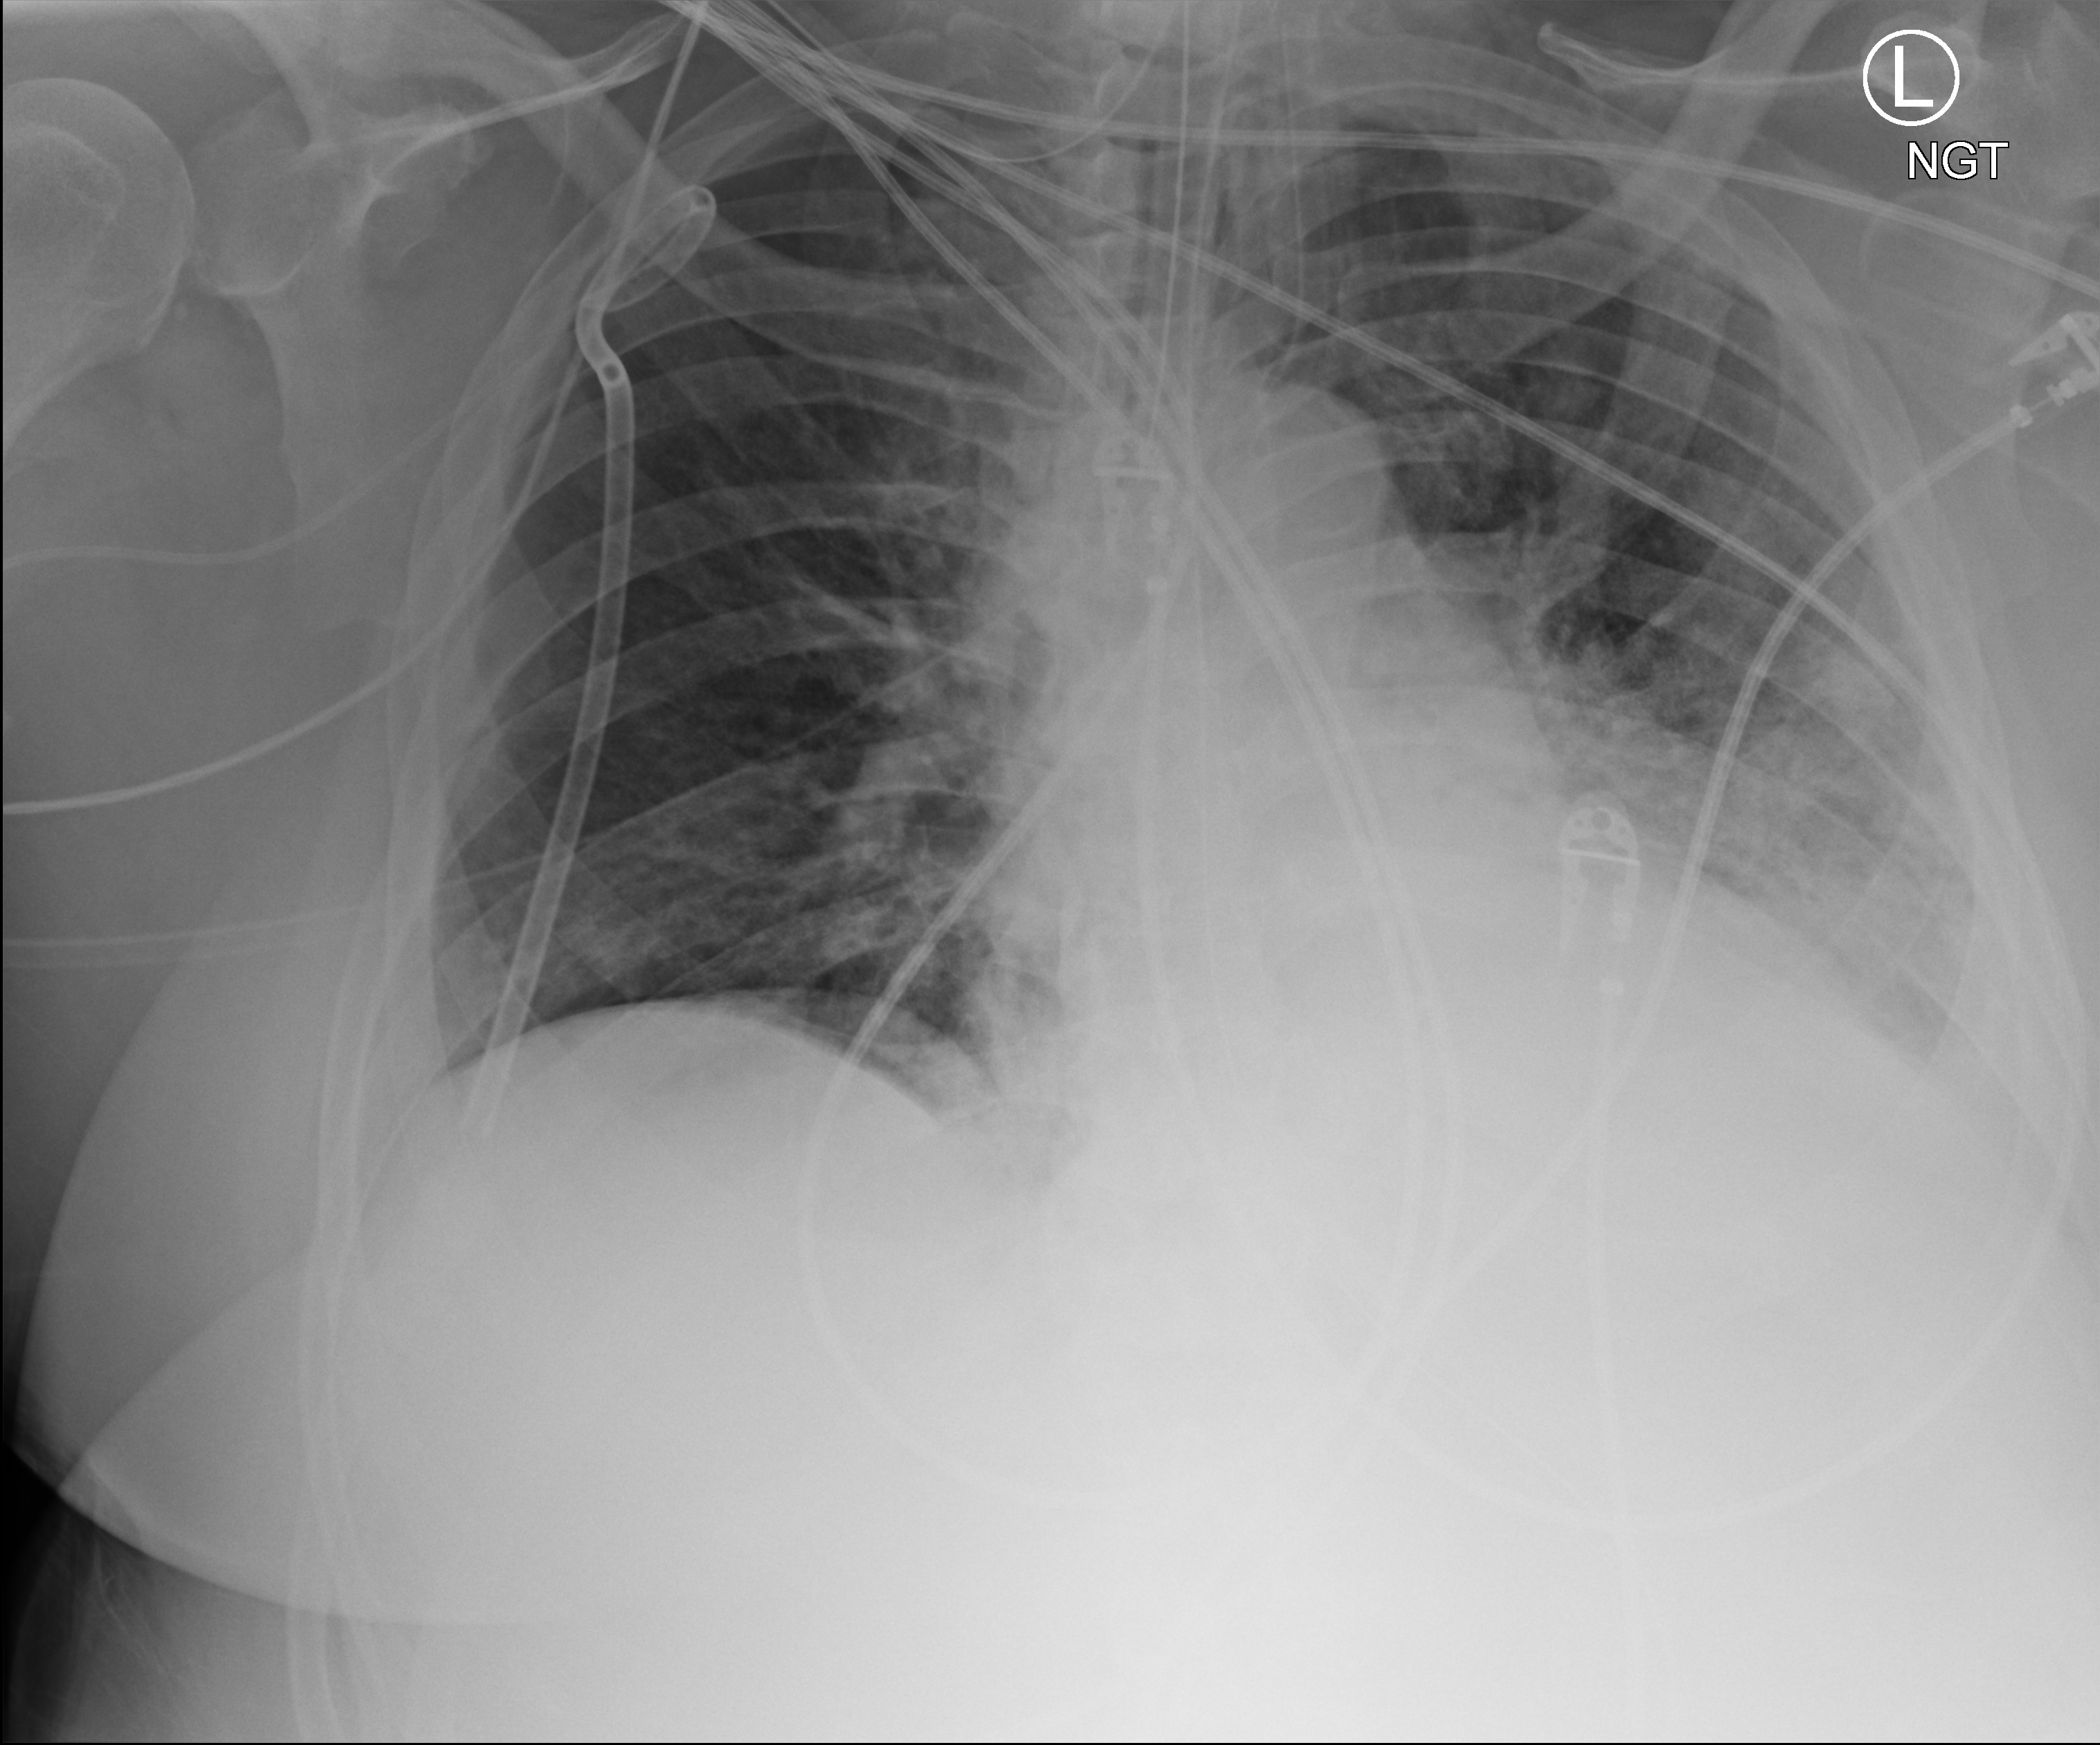
Chest X-ray (portable), anteroposterior (AP) projection. Patient hospitalised with COVID-19; male, aged 60–74 years.
Hospital-stay facts (about this admission, not read from this image; timing relative to this image not recorded):
- mechanically ventilated during this hospital stay: yes
- admitted to intensive care during this hospital stay: yes
- chronic kidney disease (admission record): no